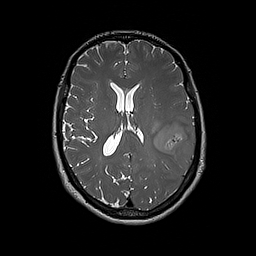
Brain MRI from a brain-tumour surgery series, one axial slice; 256 × 256 image matrix, field of view 250 × 250 mm. From the clinical record (not read from this slice): histopathology: Glioblastoma; WHO grade: 4; IDH mutation: no; tumour location: Left Frontal.
Structures marked on this image (manually delineated by an expert):
- tumour: box from (x=154, y=118) to (x=195, y=167) px